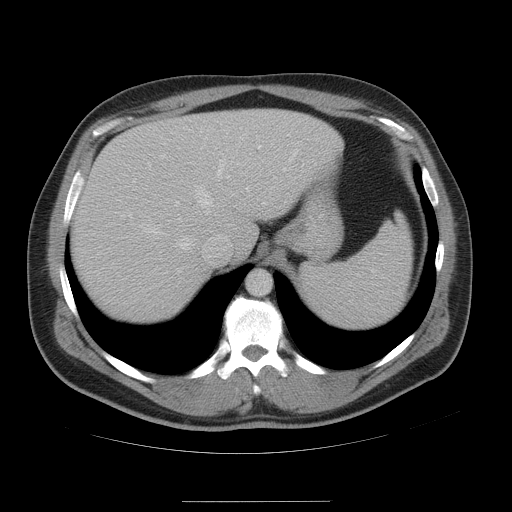
Contrast-enhanced abdominal CT, one axial slice; position 40 of 54 along the scan axis; 120 kVp; soft-tissue window (W 400 / L 40 HU); 5 mm slice thickness; 512 × 512 image matrix, field of view 436 × 436 mm. Male patient, age 40 years. From the clinical record (not read from this slice): diagnosis: colorectal cancer liver metastases, imaged before liver resection; multiple liver metastases: no; largest metastasis: 15 cm; chemotherapy before resection: no.
Annotated regions visible in this slice (outlined manually by an expert reader):
- hepatic veins: bounding box <119,152,292,252> (left, top, right, bottom; pixels)
- liver: <72,109,343,324>
- planned liver remnant (the part of the liver to remain after resection): <173,109,342,276>
- portal vein (with intrahepatic branches): <148,135,247,166>